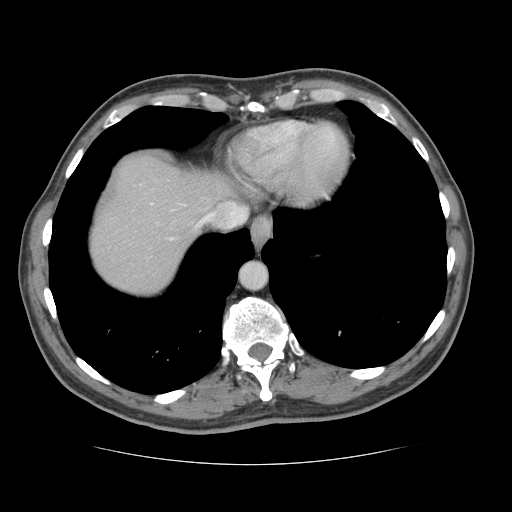
Contrast-enhanced abdominal CT, one axial slice; position 116 of 134 along the scan axis; reconstruction kernel STANDARD; 120 kVp; soft-tissue window (W 400 / L 40 HU); 2.5 mm slice thickness; 512 × 512 image matrix, field of view 377 × 377 mm. Male patient, age 68 years. Case-level facts recorded for this patient, not image findings: diagnosis: colorectal cancer liver metastases, imaged before liver resection; multiple liver metastases: yes; largest metastasis: 2.2 cm; disease in both lobes: no.
Outlined on this slice (outlined manually by an expert reader):
- hepatic veins: box from (x=151, y=202) to (x=246, y=214) px
- liver: (x=90, y=157)–(x=234, y=297)
- planned liver remnant (the part of the liver to remain after resection): (x=90, y=157)–(x=233, y=295)